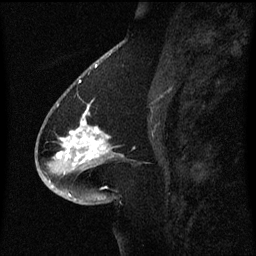
Breast MRI (dynamic contrast-enhanced), one sagittal slice. Slice 28 of 60 in the series (ordered by position). Dynamic contrast-enhanced series, image 2 of 3 at this slice position (ordered by acquisition). 1.5 T. TE 4.2 ms, TR 8.4 ms. 256 × 256 image matrix, field of view 200 × 200 mm. Female patient, age 54 years. From the clinical record (not read from this slice): setting: breast cancer imaged before/during neoadjuvant chemotherapy; receptor status: HR-positive, HER2-negative.
Outlined on this slice (semi-automatically segmented with operator editing):
- analysis volume of interest (the breast-tissue region the enhancement analysis was run in; not a lesion): bounding box [x1, y1, x2, y2] px = [46, 102, 122, 171]
- tumour enhancement mask (voxels above the 70 % enhancement threshold inside the analysis volume of interest): [58, 106, 102, 159]